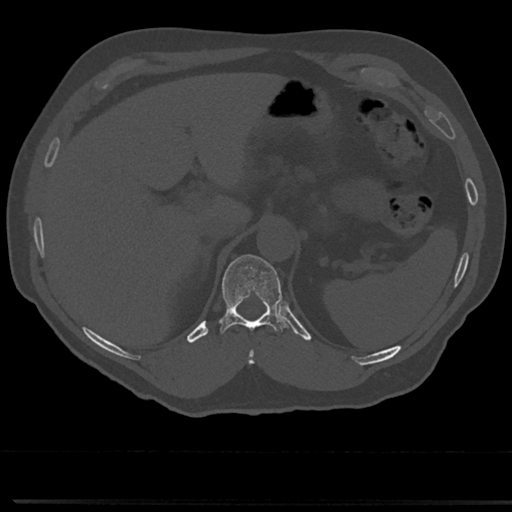
CT including the spine, one axial slice. Slice 207 of 817 in the series (ordered by position). Reconstruction kernel Br40s/3. Bone window (W 1800 / L 400 HU). 0.5 mm slice thickness. 512 × 512 image matrix, field of view 355 × 355 mm. Patient: male, 61 years. From the clinical record (not read from this slice): primary cancer: prostate.
Structures marked on this image (semi-automatically segmented with operator editing):
- T10 vertebra: bounding box [x1, y1, x2, y2] px = [246, 339, 256, 366]
- T11 vertebra: [214, 255, 290, 335]